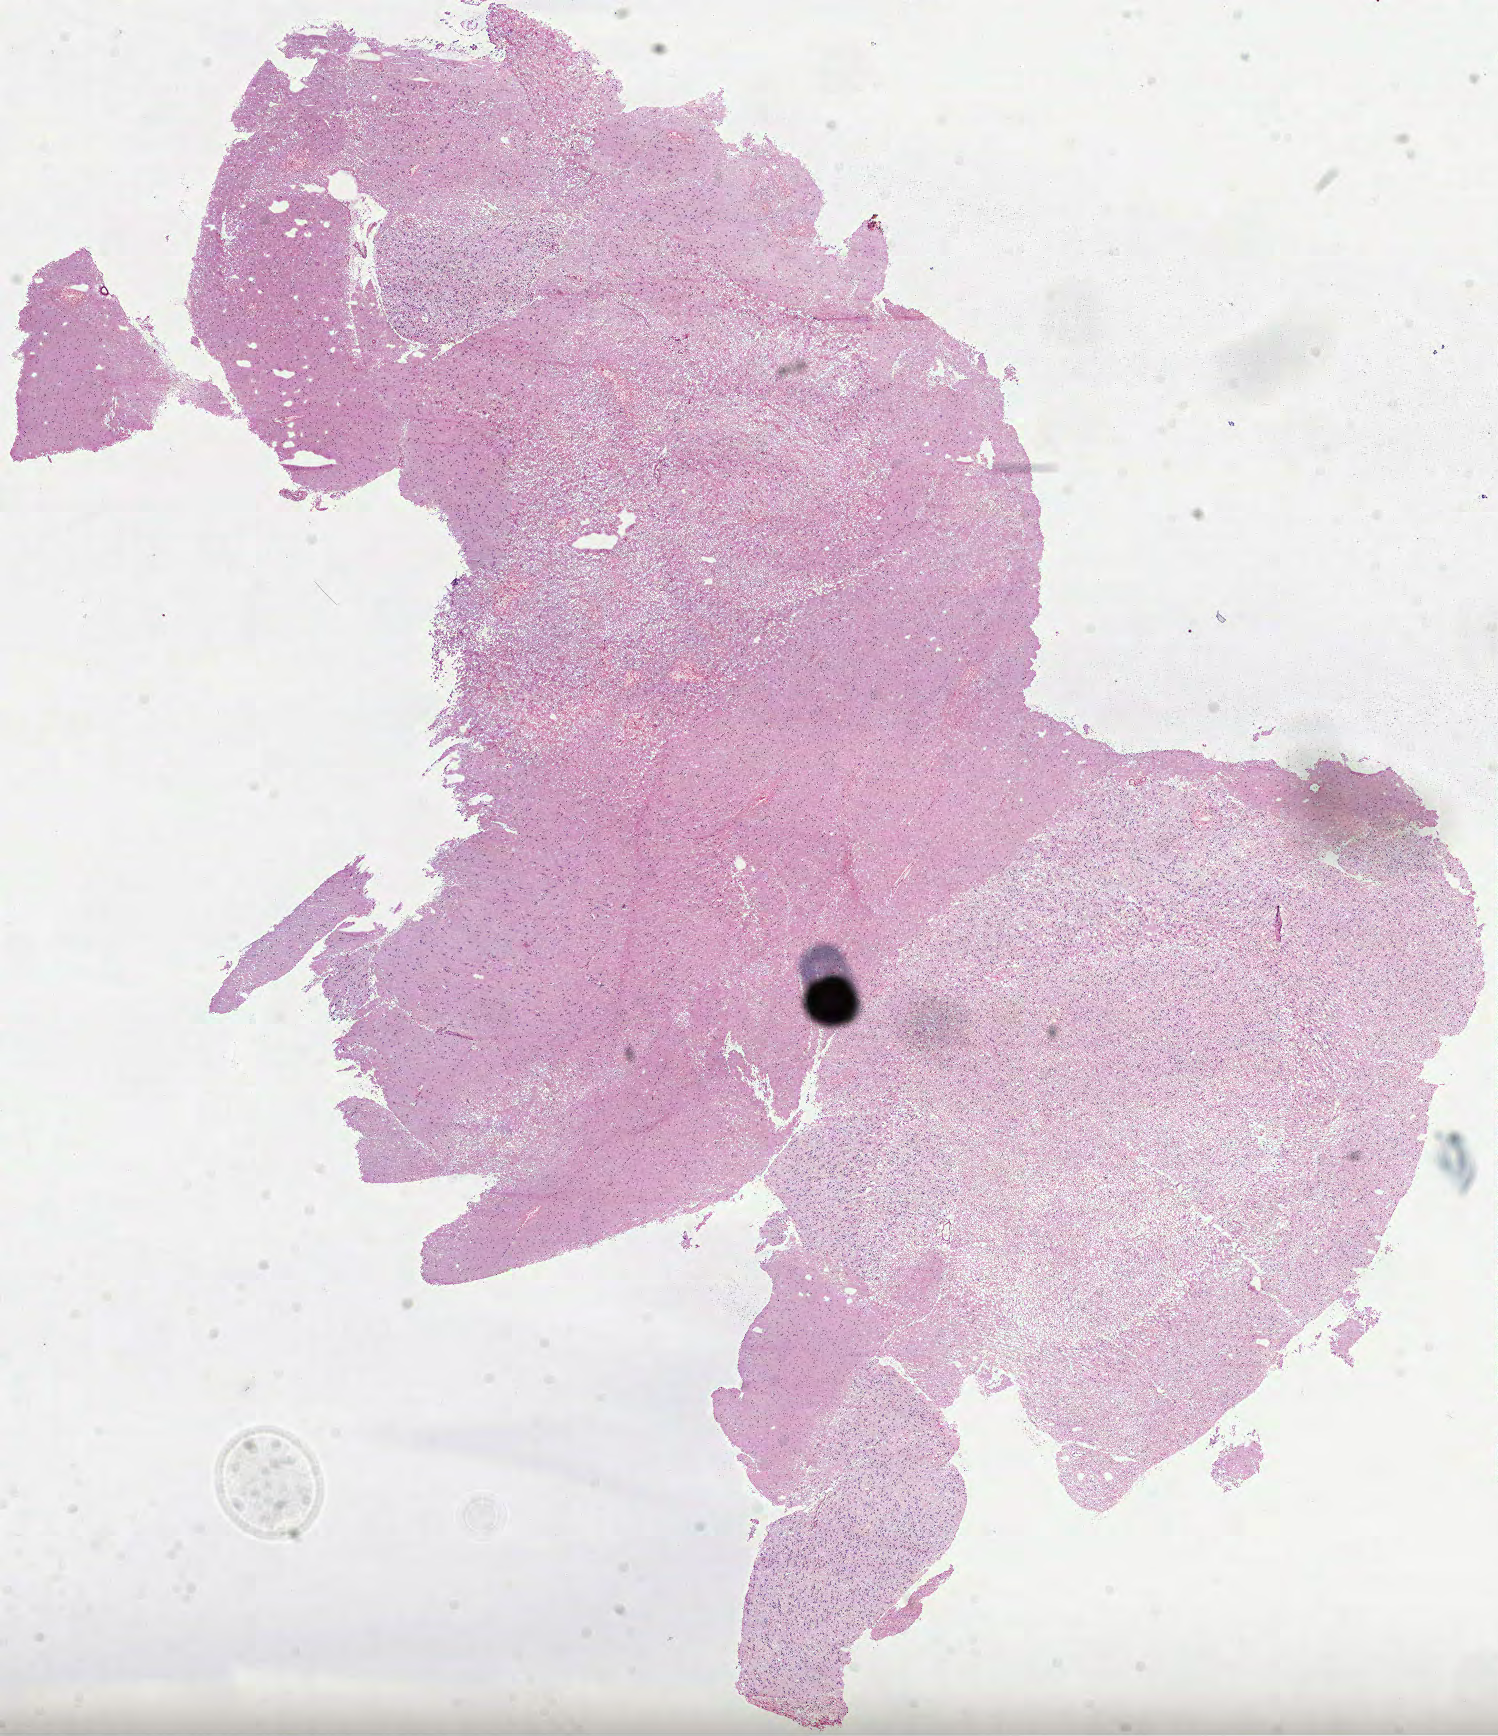
Whole-slide histology image, H&E-stained, shown as a low-resolution overview of the whole scanned area (about 12.1 x 14.0 mm, from a 40x scan); frozen section from the top of the tissue portion; sample: primary tumour, brain. Male, age 54 years at initial diagnosis.
Histologic diagnosis: Oligodendroglioma, NOS.